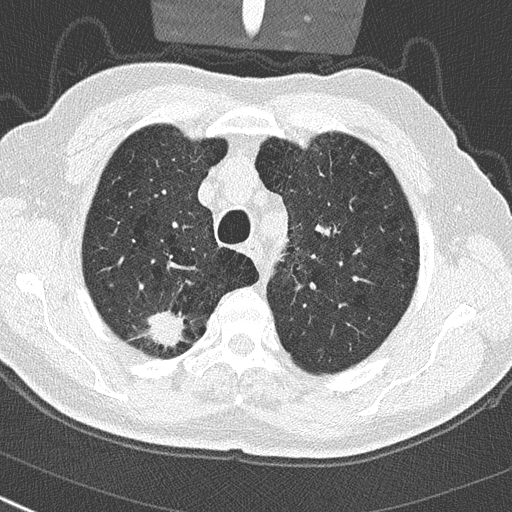
Low-dose screening chest CT, axial slice. Baseline screening round. Lung window (W 1500 / L -600 HU). 2 mm slice thickness. Lung (sharp) reconstruction kernel (B50f). Slice 60 of 290 in the series. 512 × 512 image matrix. Male, age 65 years at enrolment. Current smoker at enrolment.
- Expert-annotated lung lesion, box from (x=133, y=302) to (x=190, y=355) px.
- Screening reader's record for this exam (one nodule recorded; not confirmed to be the boxed lesion): non-calcified nodule or mass ≥4 mm, right upper lobe, 24 × 19 mm, spiculated (stellate) margins, soft tissue attenuation.
- Lung cancer was diagnosed 32 days after this screen: non-small cell carcinoma, right upper lobe, poorly differentiated (G3), stage IA (AJCC 6th edition), 29 mm at pathology.